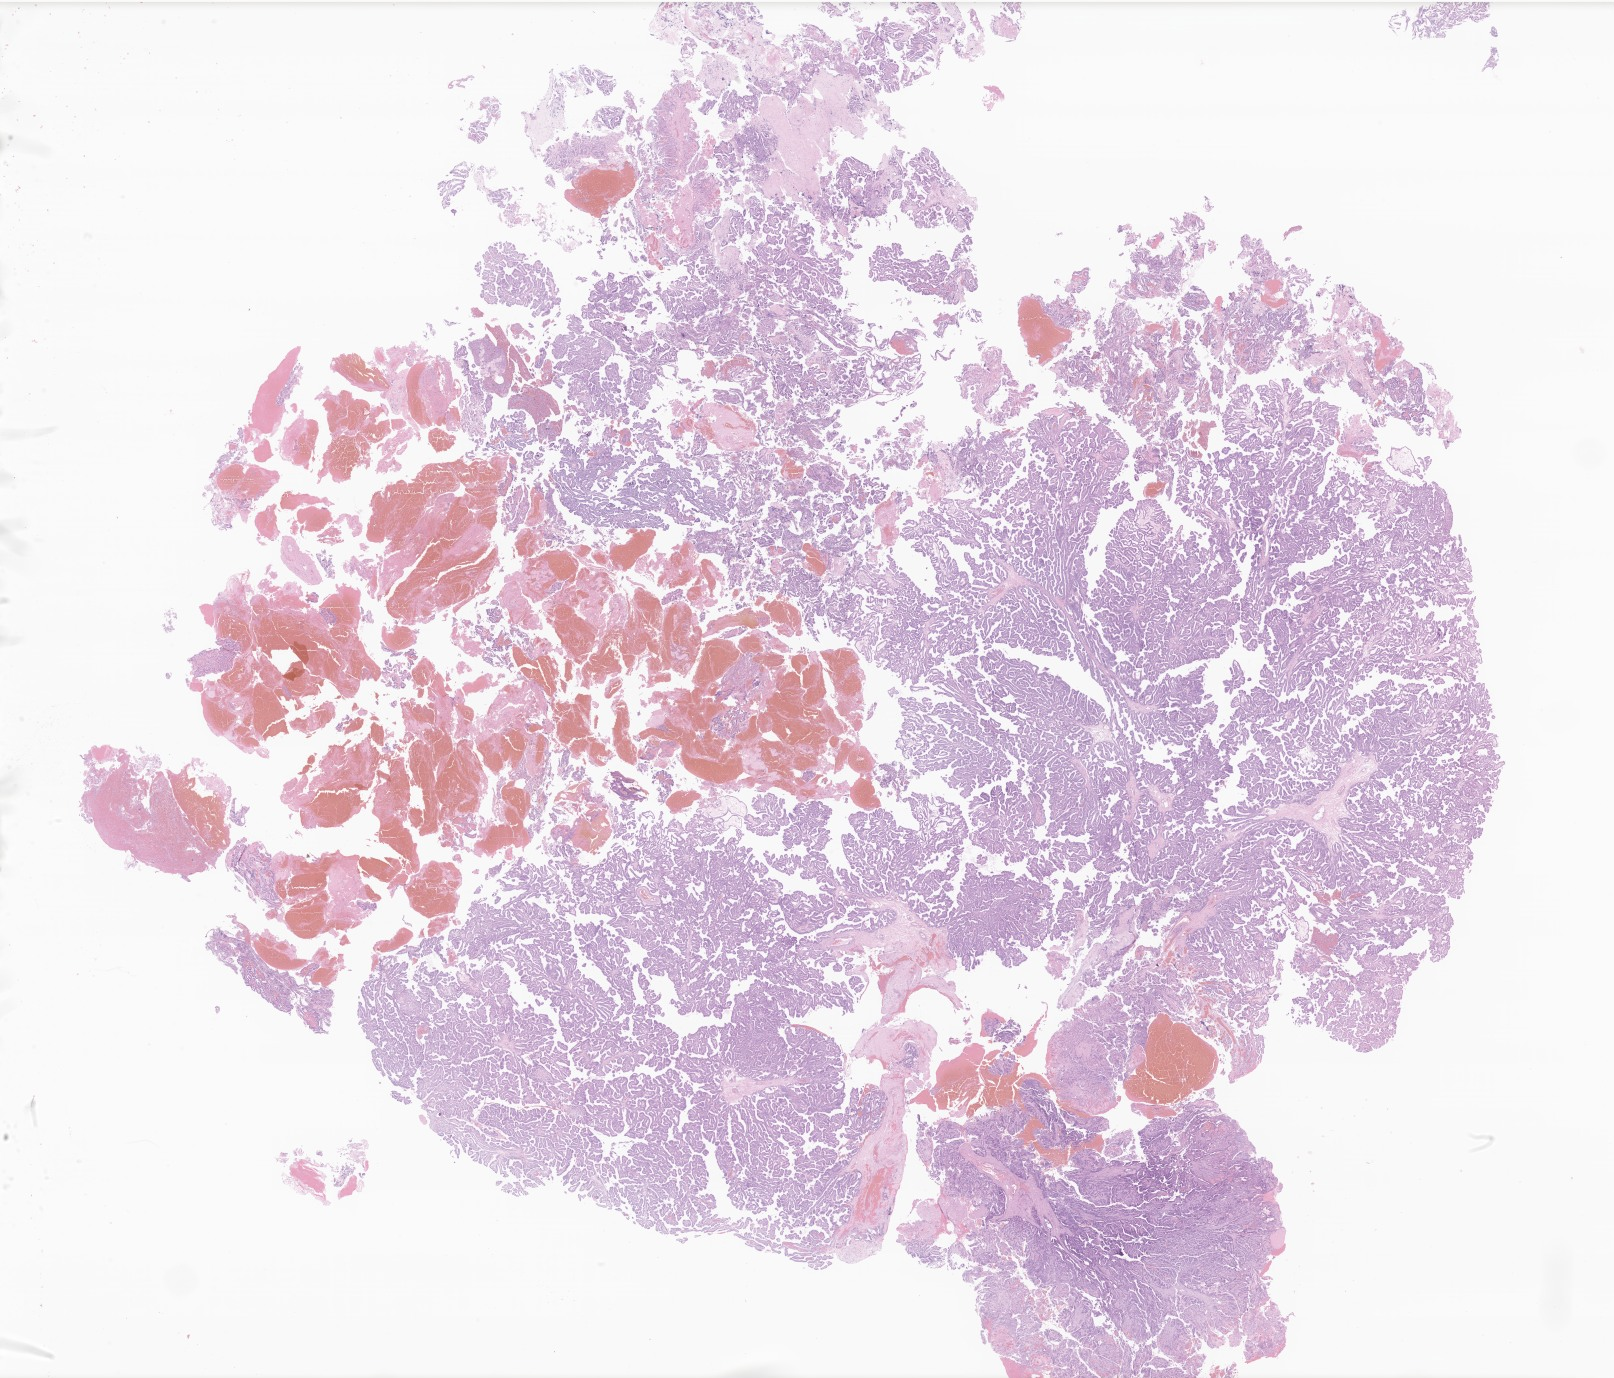
Digitized hematoxylin and eosin (H&E)-stained section of tumor tissue from the brain — a low-resolution overview of the entire scanned area, about 27.2 x 23.2 mm, formalin-fixed, paraffin-embedded (FFPE) tissue. Female patient, age 972 days (about 2.7 years).
• recorded diagnosis: Atypical choroid plexus papilloma